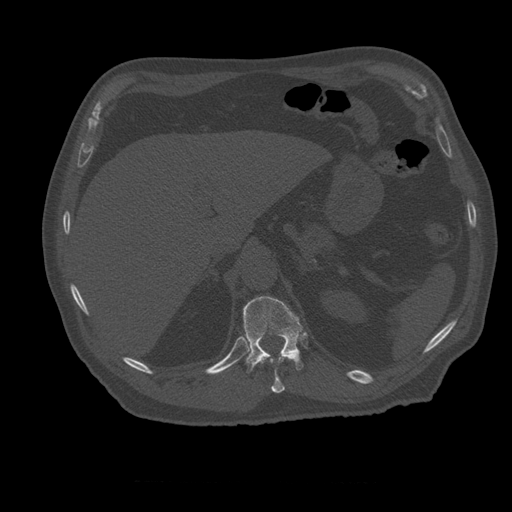
CT including the spine, one axial slice; slice 266 of 399 in the series (ordered by position); reconstruction kernel STANDARD; 120 kVp; bone window (W 1800 / L 400 HU); 512 × 512 image matrix. Patient age 73 years. Case-level facts recorded for this patient, not image findings: primary cancer: prostate; vertebrae with lytic lesions (as recorded): L2.
Outlined on this slice (semi-automatic segmentation, software-assisted and operator-edited):
- T11 vertebra: bounding box [x1, y1, x2, y2] px = [259, 352, 300, 393]
- T12 vertebra: [243, 297, 304, 373]